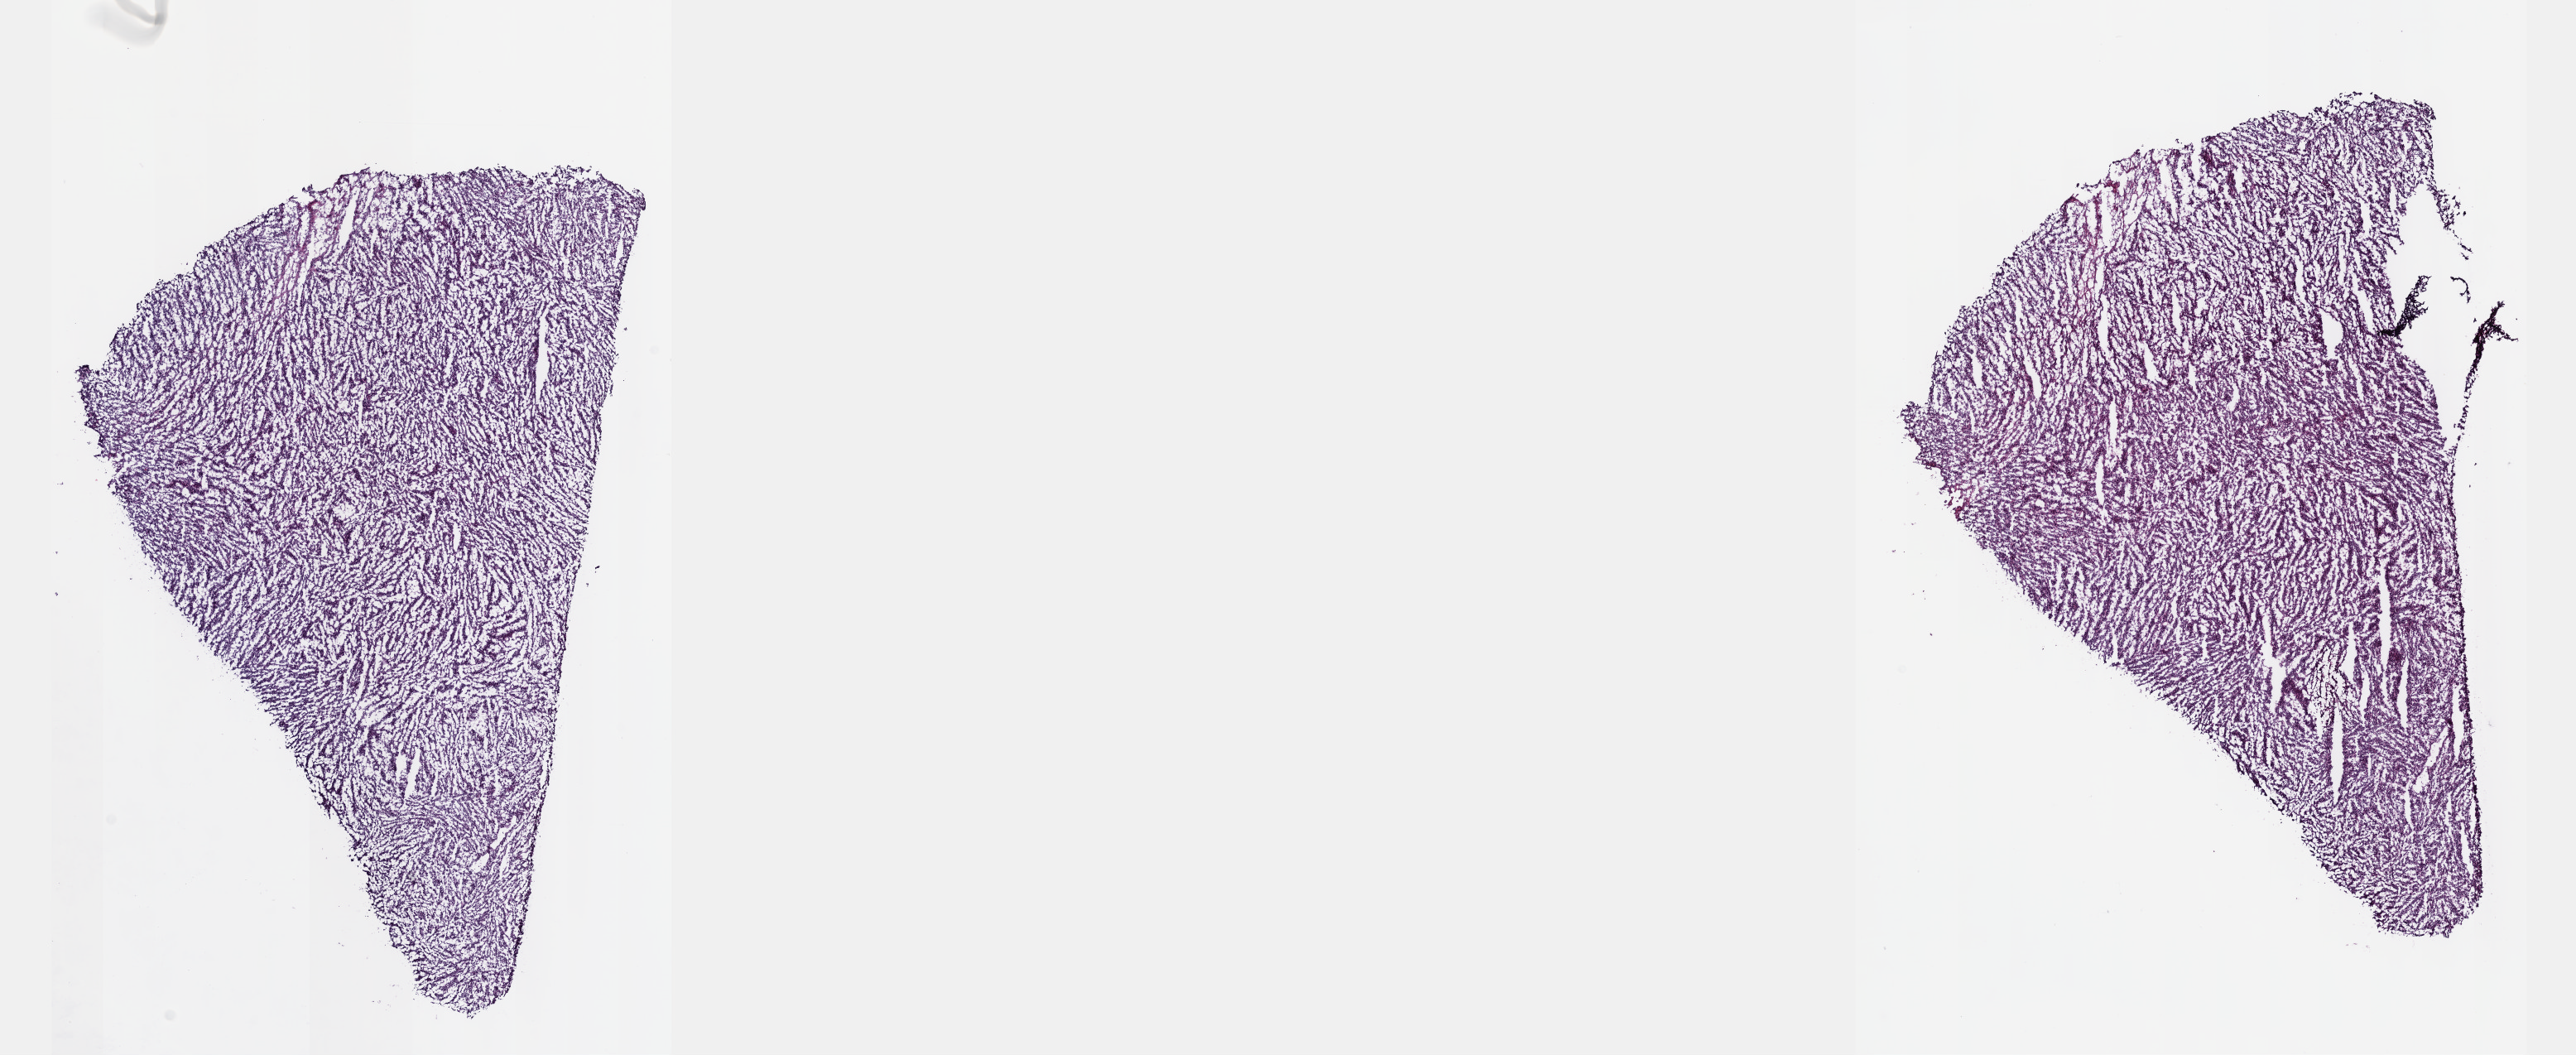
Whole-slide histology image, Hematoxylin and eosin (H&E) stained, low-resolution overview of the scanned area, about 25.1 x 10.3 mm (from a 40x scan). Frozen section from the top of the tissue portion. Connective, subcutaneous and other soft tissues, primary tumour sample. Male, age 27 years at initial diagnosis. Slide review estimates, as recorded: tumour cells 100%, tumour nuclei 95%, normal cells 0%, stromal cells 0%, necrosis 0%. Inflammatory infiltration, as recorded: lymphocyte infiltration 0%, monocyte infiltration 0%, neutrophil infiltration 0%.
Histologic diagnosis: Synovial sarcoma, spindle cell (connective, subcutaneous and other soft tissues of lower limb and hip).